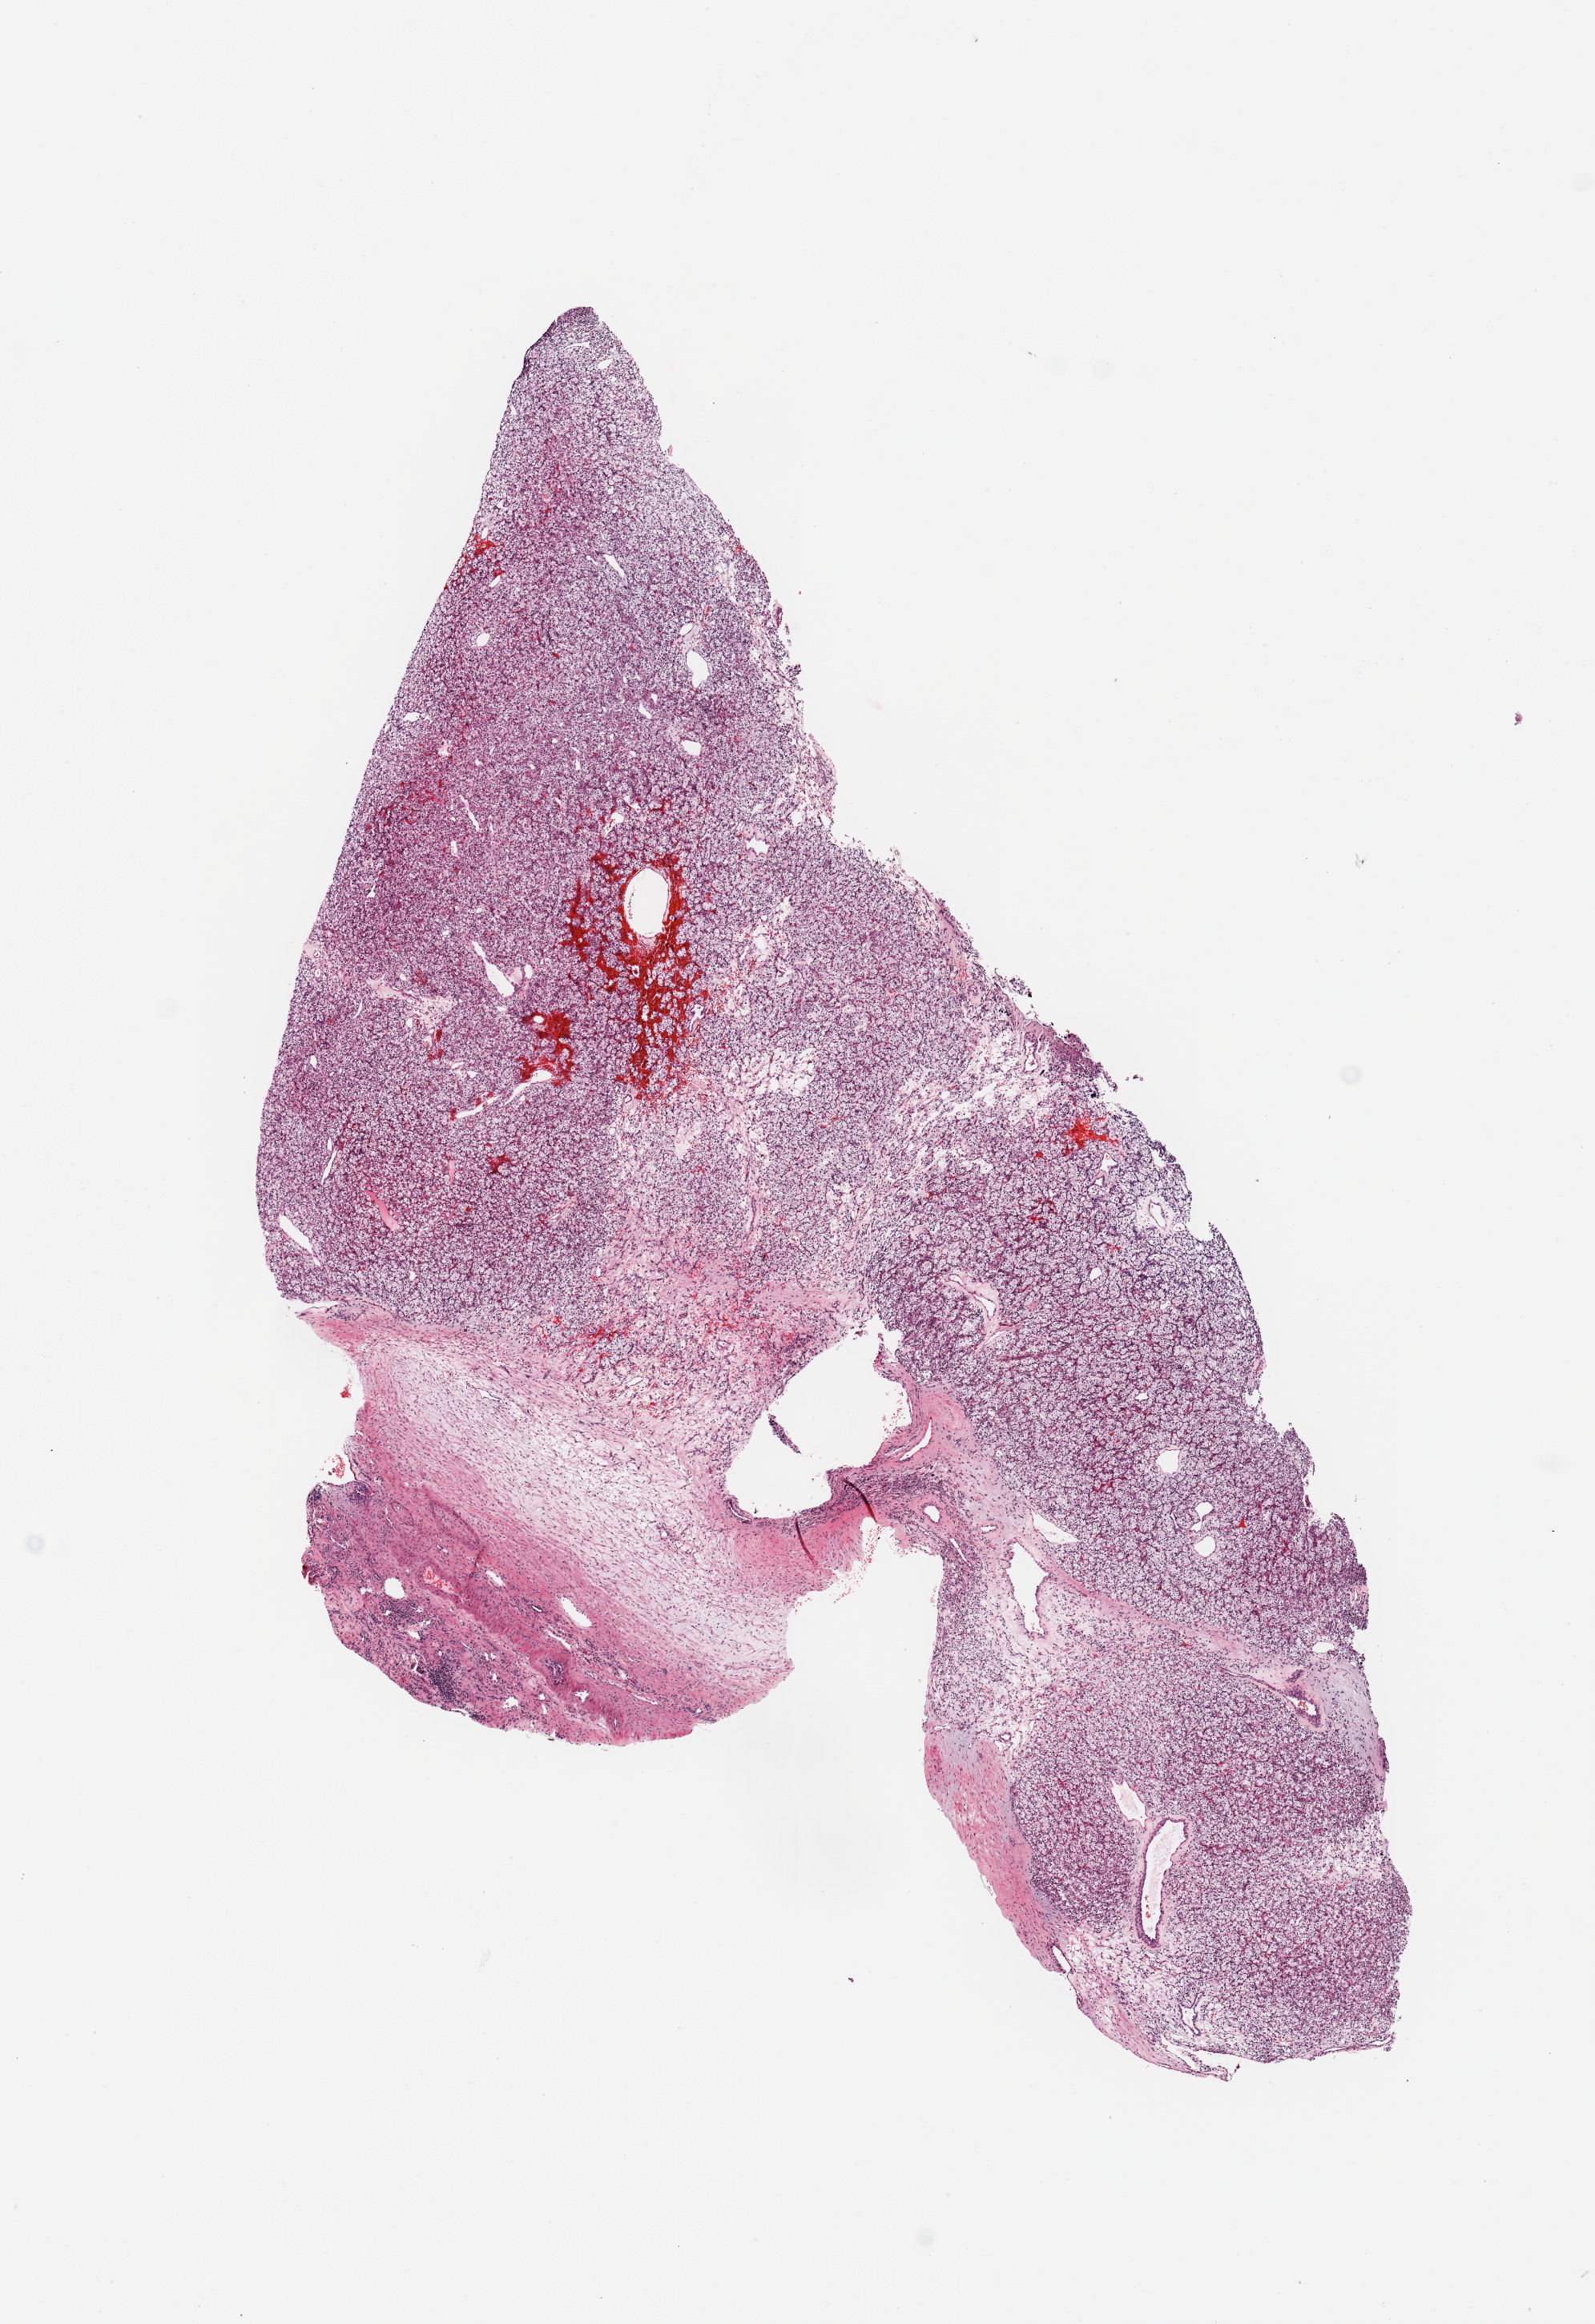
Whole-slide histology image, H&E, a low-resolution overview of the entire scanned area, about 7.9 x 11.5 mm. Tumour tissue sample, sampled site: kidney. 59-year-old male patient. Histologic grade: G2 (moderately differentiated). Composition of this section per pathologist review: tumour nuclei 80%, necrosis 0%.
Histologic diagnosis: Renal cell carcinoma, NOS. Primary tumour site (as recorded): upper pole. AJCC pathologic stage: I.